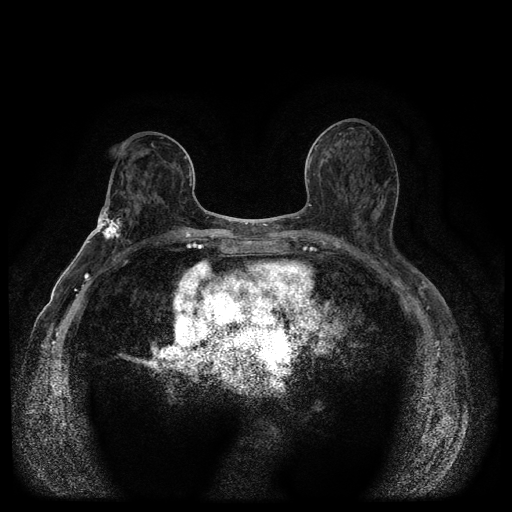
Breast MRI (dynamic contrast-enhanced, multi-phase), one axial slice. Slice 51 of 116 in the series (ordered by position). Dynamic contrast-enhanced series, time point 2 of 5 at this slice position (early post-contrast). 1.5 T. TE 2.7 ms, TR 5.4 ms. 512 × 512 image matrix, field of view 340 × 340 mm. Female patient, age 75 years.
Outlined on this slice (semi-automatic segmentation, software-assisted and operator-edited):
- breast lesion (labelled 'tumour' in the annotation; benign lesions carry a separate 'benign' label): bounding box (x1, y1, x2, y2) in pixels: (90, 200, 125, 243)